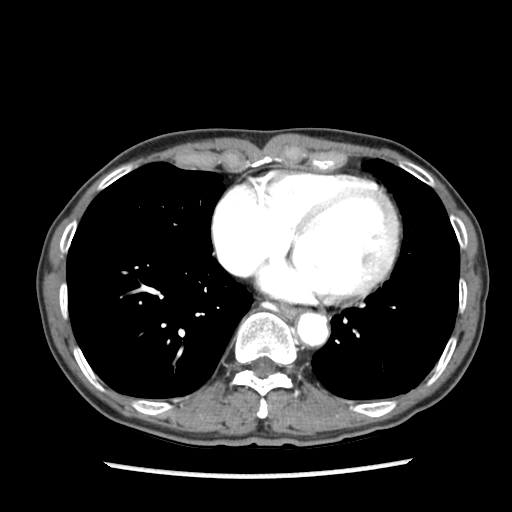
Contrast-enhanced abdominal CT (liver protocol), one axial slice. Position 85 of 87 along the scan axis. 140 kVp. Soft-tissue window (W 400 / L 40 HU). 2.5 mm slice thickness. 512 × 512 image matrix, field of view 300 × 300 mm. From the clinical record (not read from this slice): diagnosis: hepatocellular carcinoma (patient treated with transarterial chemoembolisation; whether this scan precedes or follows treatment is not stated here); TNM stage (as recorded): Stage-IIIB; Child-Pugh class: A; tumour differentiation: well differentiated; tumour nodularity: uninodular.
Structures marked on this image (semi-automatically segmented with operator editing):
- abdominal aorta: box from (x=298, y=313) to (x=327, y=344) px